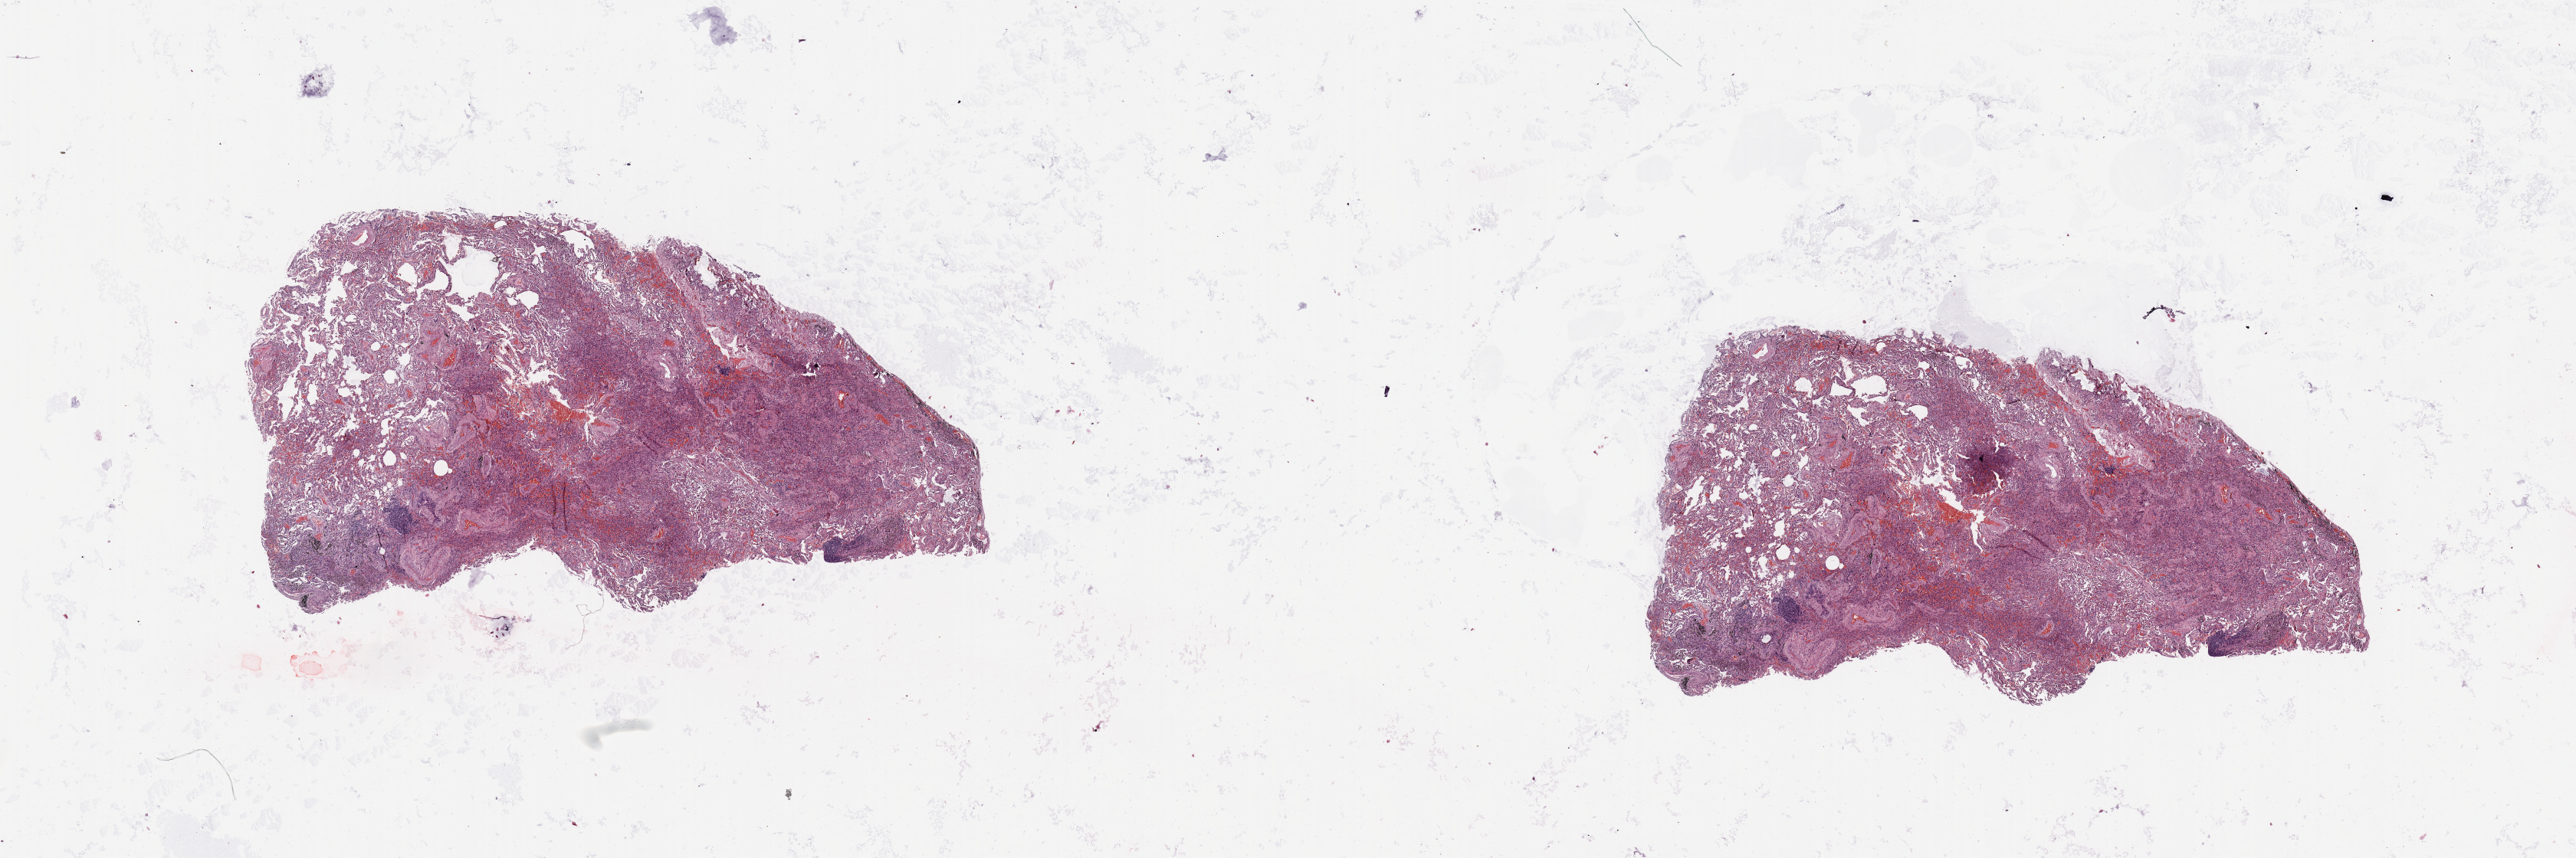
Digitized H&E-stained tissue section (whole slide), a low-resolution overview of the entire scanned area, about 26.6 x 8.9 mm (slide scanned at 20x). Normal (non-tumour) tissue sample, lung. 63-year-old male patient.
This section: normal (non-tumour) tissue from the same patient. Patient diagnosis (cohort enrolment): squamous cell carcinoma (lung).